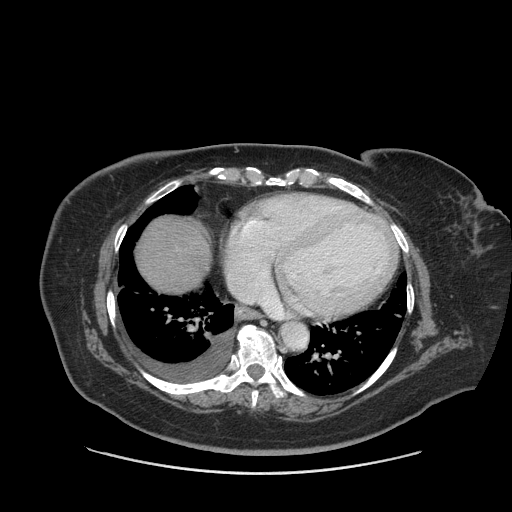
Contrast-enhanced abdominal CT (liver protocol), one axial slice; position 83 of 91 along the scan axis; 140 kVp; soft-tissue window (W 400 / L 40 HU); 512 × 512 image matrix, field of view 420 × 420 mm. From the clinical record (not read from this slice): diagnosis: hepatocellular carcinoma (patient treated with transarterial chemoembolisation; whether this scan precedes or follows treatment is not stated here); TNM stage (as recorded): Stage-I; Child-Pugh class: A; tumour differentiation: well differentiated.
Outlined on this slice (semi-automatically segmented with operator editing):
- liver parenchyma outside the tumour (the mass and vessels are separate outlines, so this box may not span the whole liver): bounding box <134,214,210,292> (left, top, right, bottom; pixels)